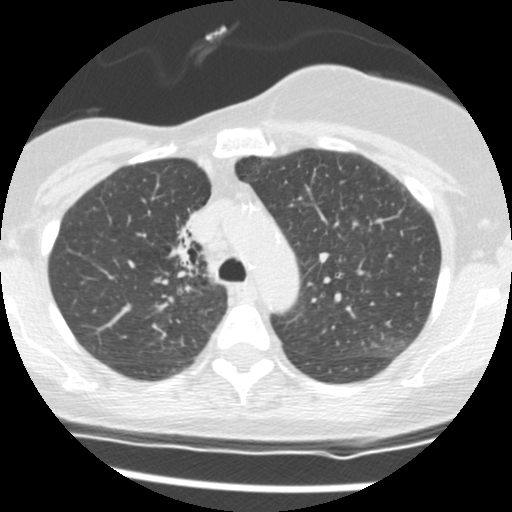
Chest CT (low-dose screening protocol), one axial image. Second screening round (one year after baseline). Lung window (W 1500 / L -600 HU). 2.5 mm slice thickness. 512 × 512 image matrix, field of view 296 × 296 mm. Female participant, aged 56 years at enrolment.
Expert reader's lesion annotation, bounding box (x1, y1, x2, y2) in pixels: (155, 204, 215, 279). The screening reader recorded 2 non-calcified nodules or masses ≥4 mm on this exam (right middle lobe, right lower lobe); which of them this box marks is not recorded. Official screen result: positive, change unspecified: nodule(s) >= 4 mm or enlarging nodule(s), mass(es), or other non-specific abnormalities suspicious for lung cancer. Lung cancer was diagnosed 675 days after this screen (after the third annual screen): adenocarcinoma, NOS, right upper lobe, stage IIIB (AJCC 6th edition), 8 mm at pathology.